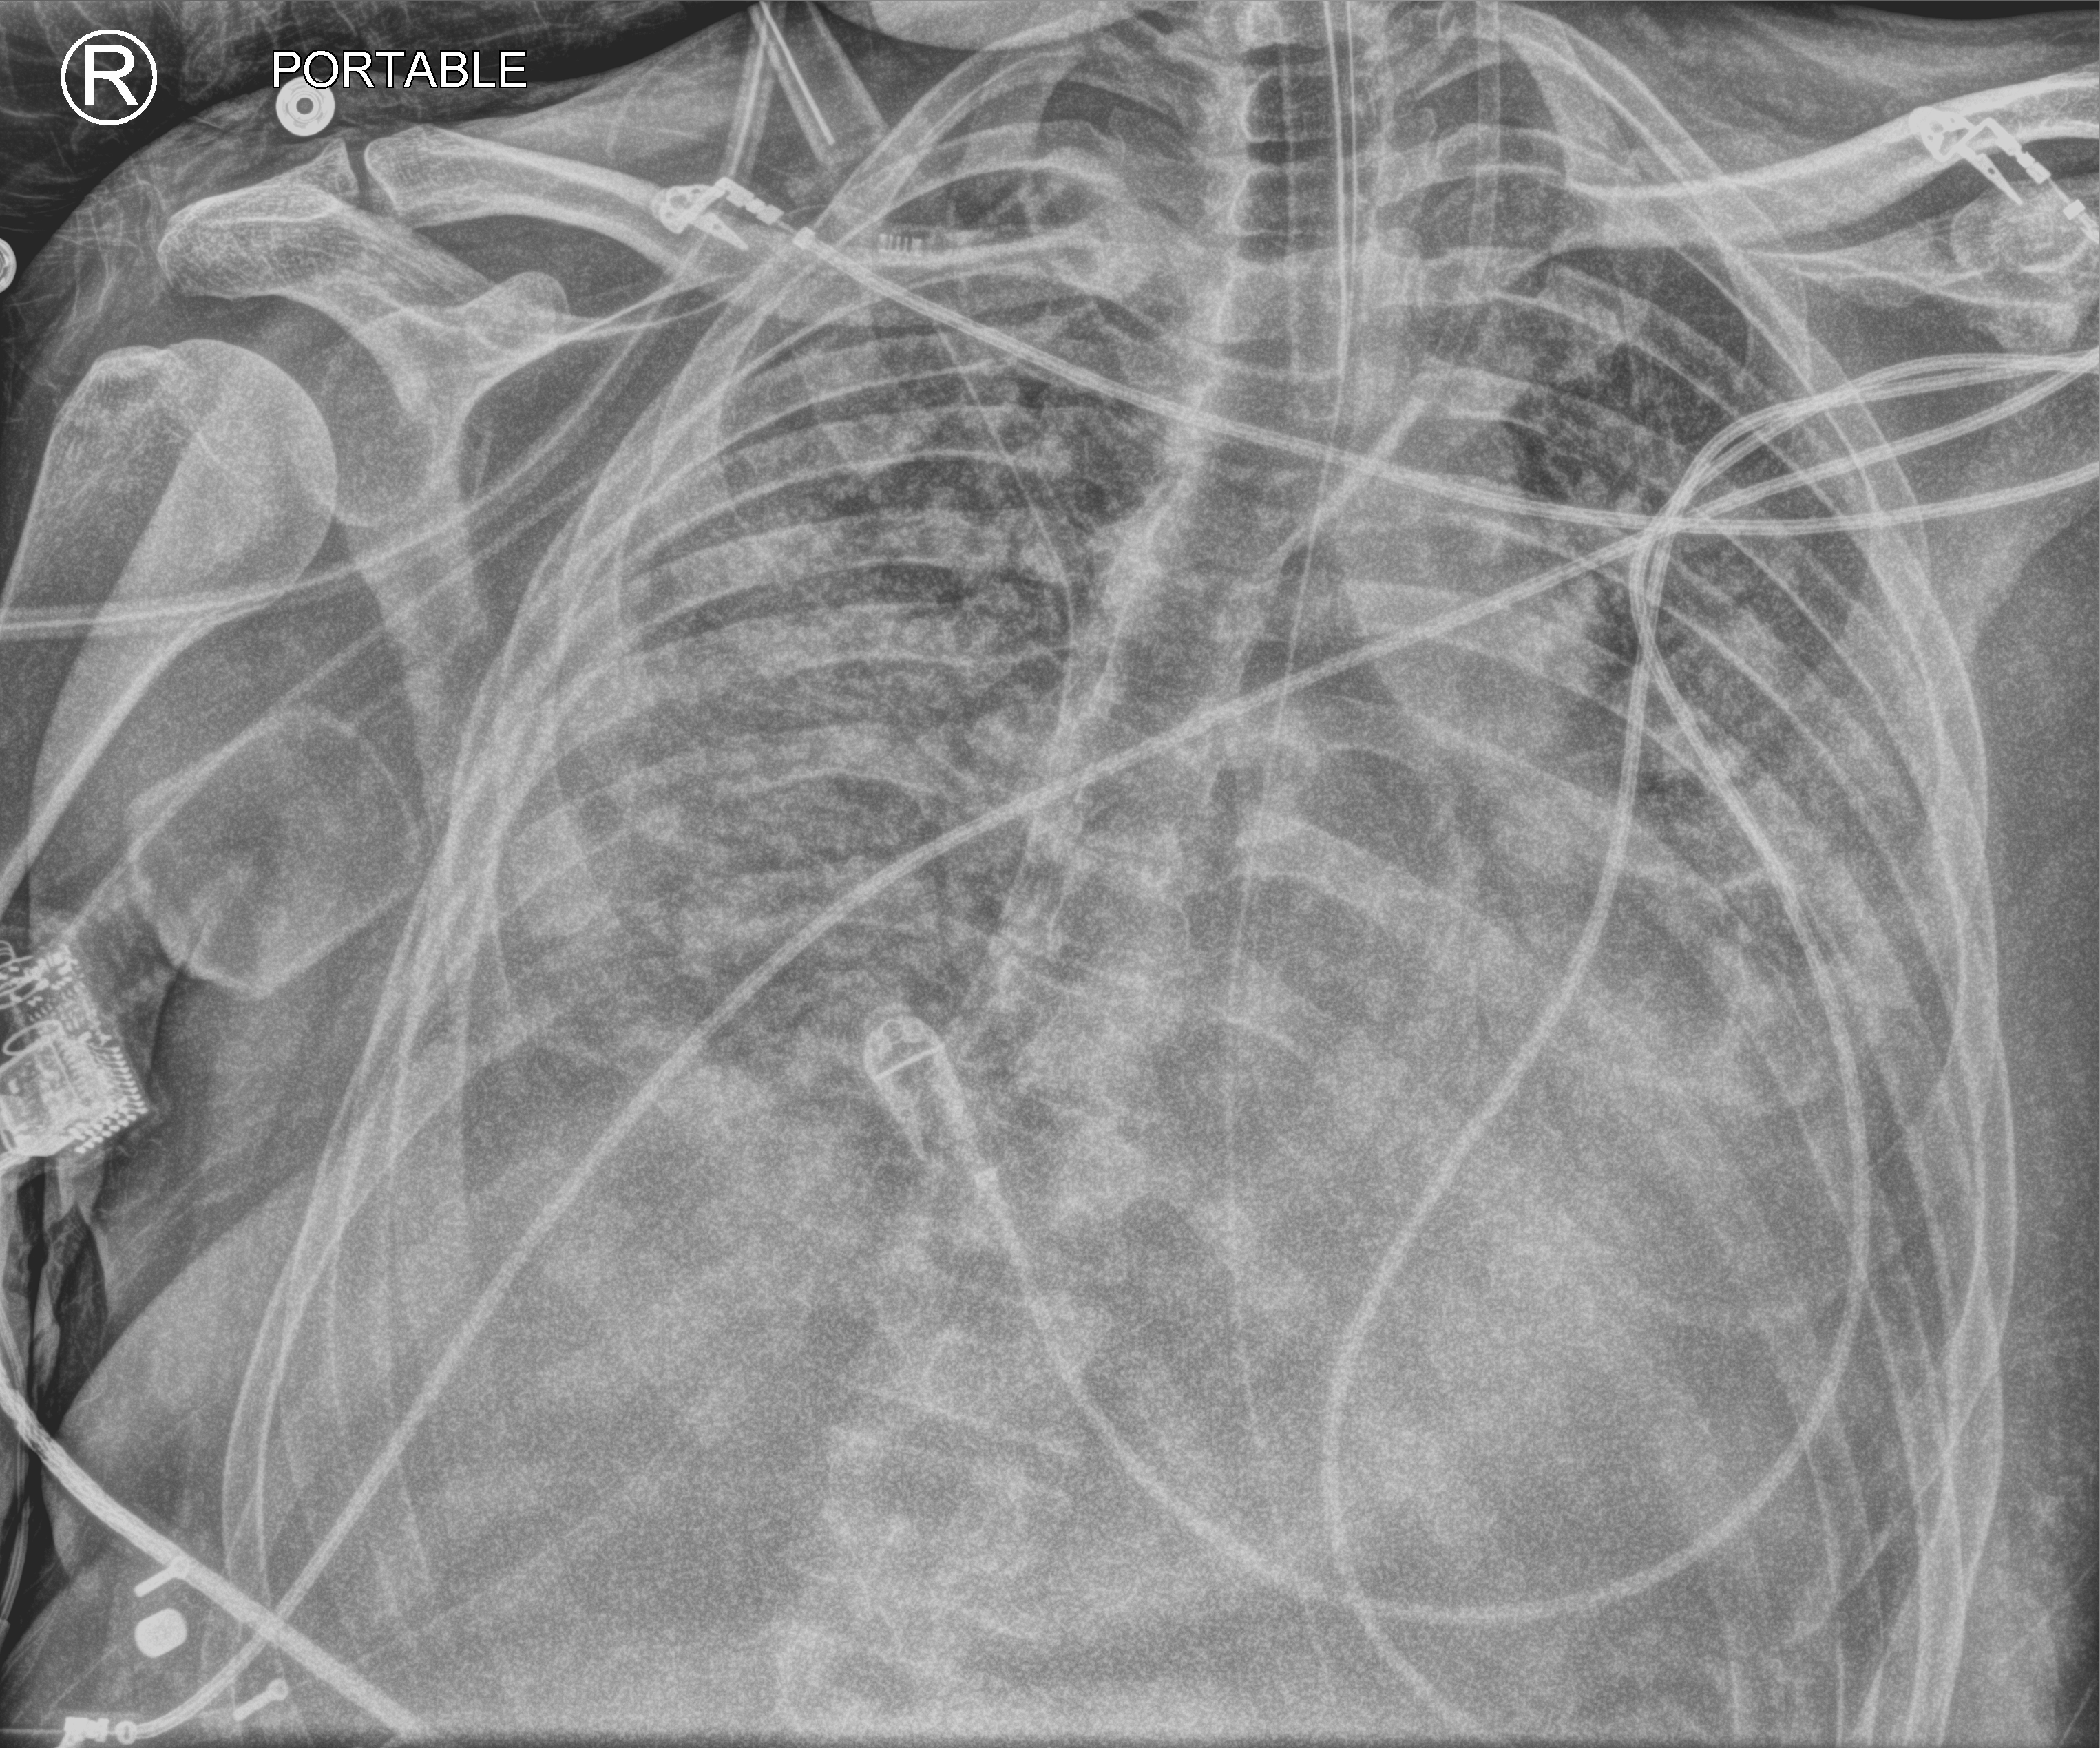
Chest X-ray (portable); anteroposterior (AP) projection. Patient hospitalised with COVID-19; male, aged 18–59 years.
Hospital-stay facts (about this admission, not read from this image; timing relative to this image not recorded):
- admitted to intensive care during this hospital stay: yes
- mechanically ventilated during this hospital stay: yes